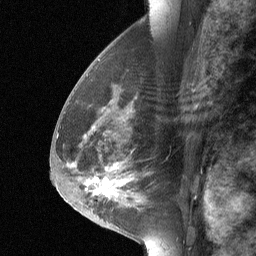
Breast MRI (dynamic contrast-enhanced), one sagittal slice. Slice 33 of 64 in the series (ordered by position). Dynamic contrast-enhanced study with each time point stored as its own series, time point 2 of 3 at this slice position (early post-contrast, ordered by acquisition time). 1.5 T. TE 4.8 ms, TR 27 ms. 2 mm slice thickness. 256 × 256 image matrix, field of view 180 × 180 mm. Female patient, age 56 years. Case-level facts recorded for this patient, not image findings: setting: breast cancer imaged before/during neoadjuvant chemotherapy; receptor status: HER2-positive.
Structures marked on this image (semi-automatic segmentation, software-assisted and operator-edited):
- analysis volume of interest (the breast-tissue region the enhancement analysis was run in; not a lesion): box from (x=68, y=83) to (x=146, y=214) px
- tumour enhancement mask (voxels above the 90 % enhancement threshold inside the analysis volume of interest): (x=89, y=165)–(x=127, y=195)